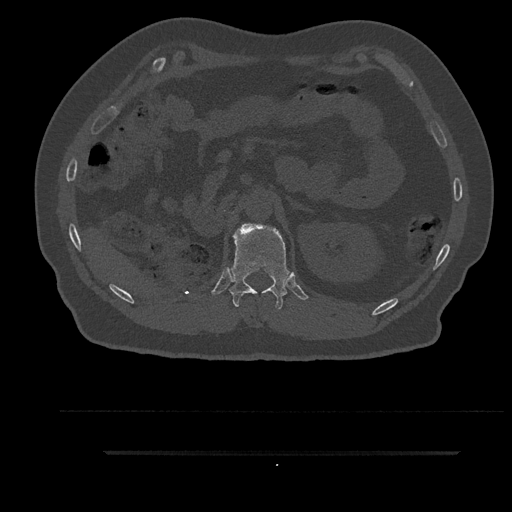
CT including the spine, one axial slice; position 243 of 797 along the scan axis; bone window (W 1800 / L 400 HU); 0.5 mm slice thickness; 512 × 512 image matrix. Male patient, age 63 years. From the clinical record (not read from this slice): primary cancer: renal; vertebrae with lytic lesions (as recorded): T8.
Outlined on this slice (semi-automatic segmentation, software-assisted and operator-edited):
- T12 vertebra: bounding box (x1, y1, x2, y2) in pixels: (229, 224, 290, 309)